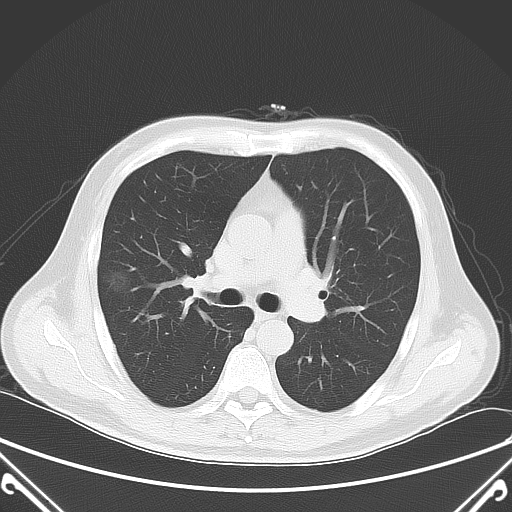
Chest CT, one axial slice. Position 46 of 72 along the scan axis. Lung window (W 1500 / L -600 HU). 5 mm slice thickness. 512 × 512 image matrix. Patient: male, 64 years. From the clinical record (not read from this slice): clinical TNM (as recorded): T1c N0 M0; histopathological grade: G2.
Outlined on this slice (rectangle marked by the reading radiologist):
- lung tumour (recorded histology: adenocarcinoma): box from (x=100, y=268) to (x=137, y=302) px